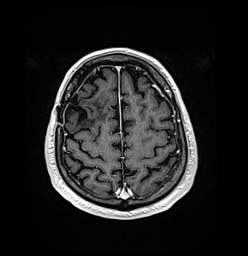
Brain MRI from a brain-tumour surgery series, one axial slice. Slice 39 of 176 in the series (ordered by position). T1-weighted post-contrast. 1 mm slice thickness. 248 × 256 image matrix, field of view 242 × 250 mm. Case-level facts recorded for this patient, not image findings: histopathology: Oligodendroglioma; WHO grade: 3; IDH mutation: yes; tumour location: Right Frontal.
Outlined on this slice (expert manual segmentation):
- previous resection cavity: bounding box <67,94,89,125> (left, top, right, bottom; pixels)